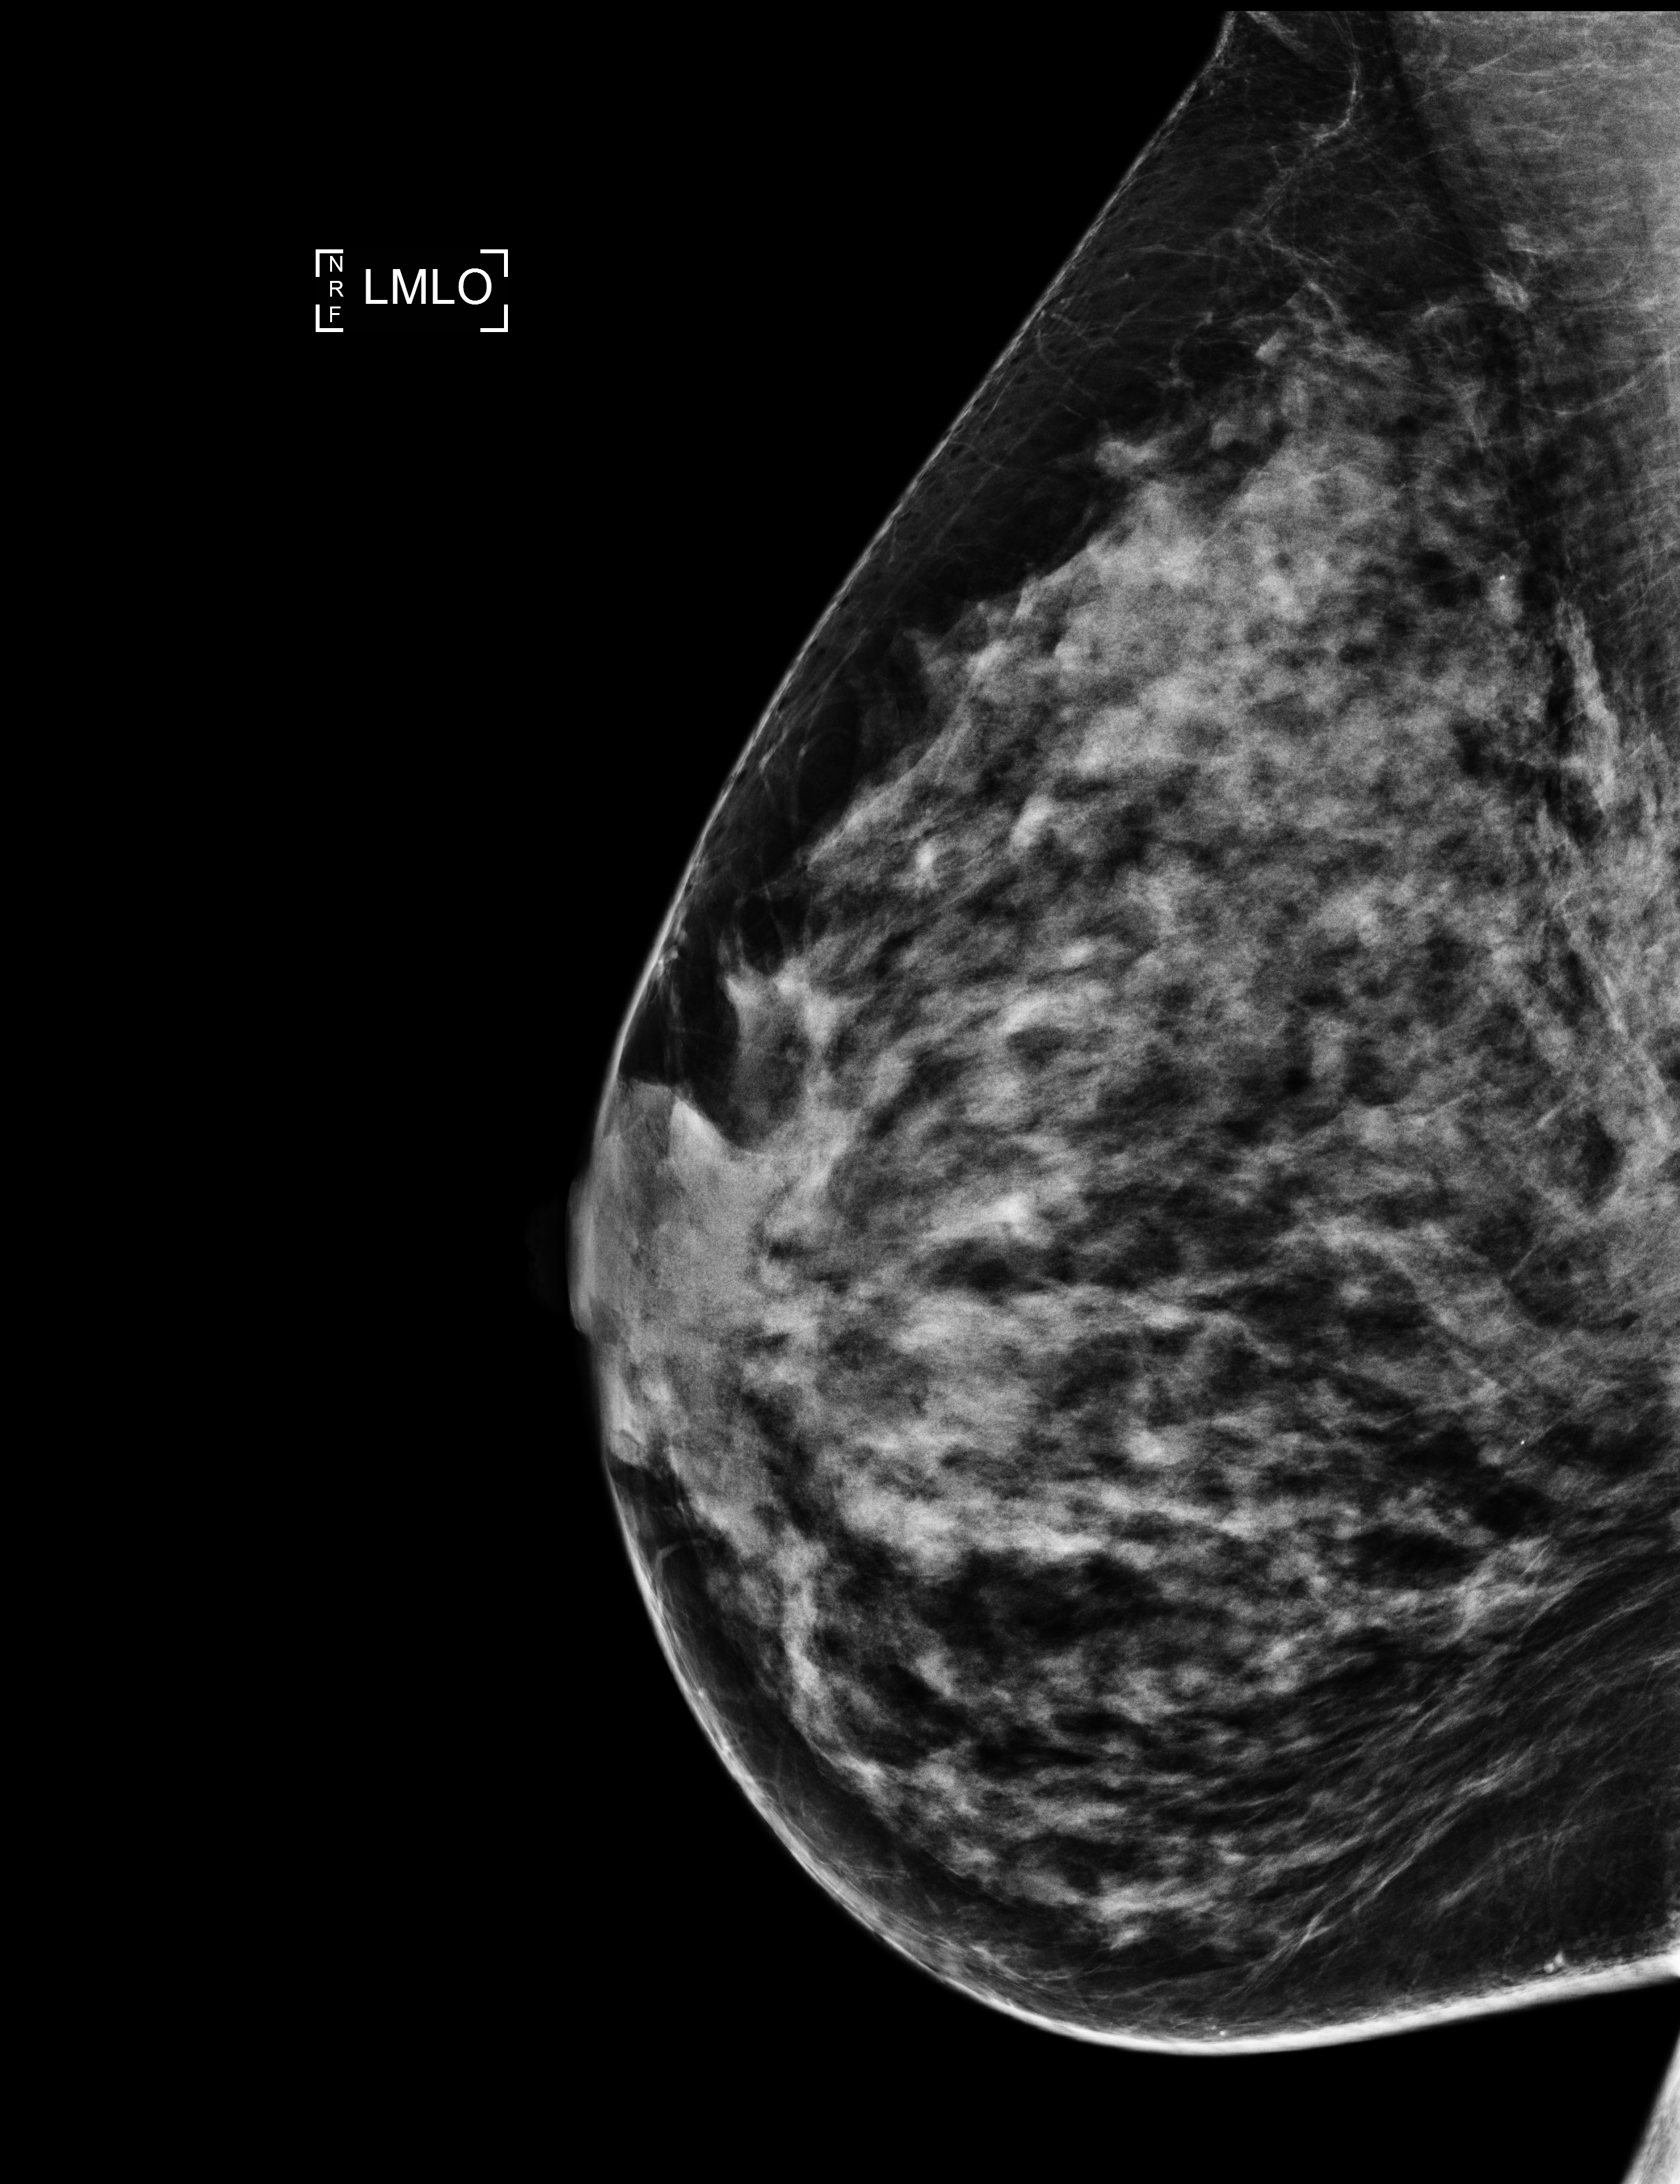
Annual screening mammography examination; compressed breast thickness 61 mm; system: Selenia Dimensions. Female patient, age 60 years.
Image type: full-field digital mammogram. Breast: left. Projection: medio-lateral oblique projection. BI-RADS breast density category at the screening exam (both breasts, scale 1–4): 4. Final BI-RADS assessment for this screening round (tomosynthesis exam, both breasts): category 1. Recall: no recall after this screen.